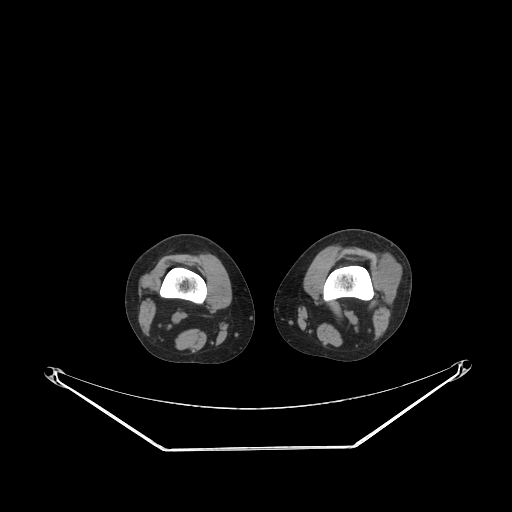
CT of an extremity soft-tissue mass (from a PET/CT study), one axial slice; position 171 of 223 along the scan axis; soft-tissue window (W 400 / L 40 HU); 3.75 mm slice thickness; 512 × 512 image matrix. Female patient. From the clinical record (not read from this slice): histological type: spindle cell suggestive of biphasic synovial sarcoma; grade: intermediate; site of the primary tumour: left knee.
Annotated regions visible in this slice (expert contour drawn on MRI and transferred to this co-registered scan by the dataset authors):
- gross tumour volume including surrounding oedema: bounding box <374,253,401,302> (left, top, right, bottom; pixels)
- gross tumour volume (mass): <374,256,401,302>